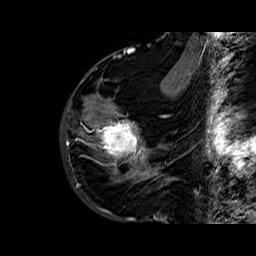
Breast MRI (dynamic contrast-enhanced), one sagittal slice; position 18 of 60 along the scan axis; dynamic contrast-enhanced series, time point 2 of 6 at this slice position (early post-contrast); 1.5 T; TE 6.4 ms, TR 32.8 ms; 256 × 256 image matrix. Female patient. Case-level facts recorded for this patient, not image findings: setting: breast cancer imaged before/during neoadjuvant chemotherapy; receptor status: HR-positive, HER2-negative.
Annotated regions visible in this slice (semi-automatically segmented with operator editing):
- analysis volume of interest (the breast-tissue region the enhancement analysis was run in; not a lesion): bounding box (x1, y1, x2, y2) in pixels: (86, 78, 163, 177)
- tumour enhancement mask (voxels above the 100 % enhancement threshold inside the analysis volume of interest): (86, 99, 156, 175)